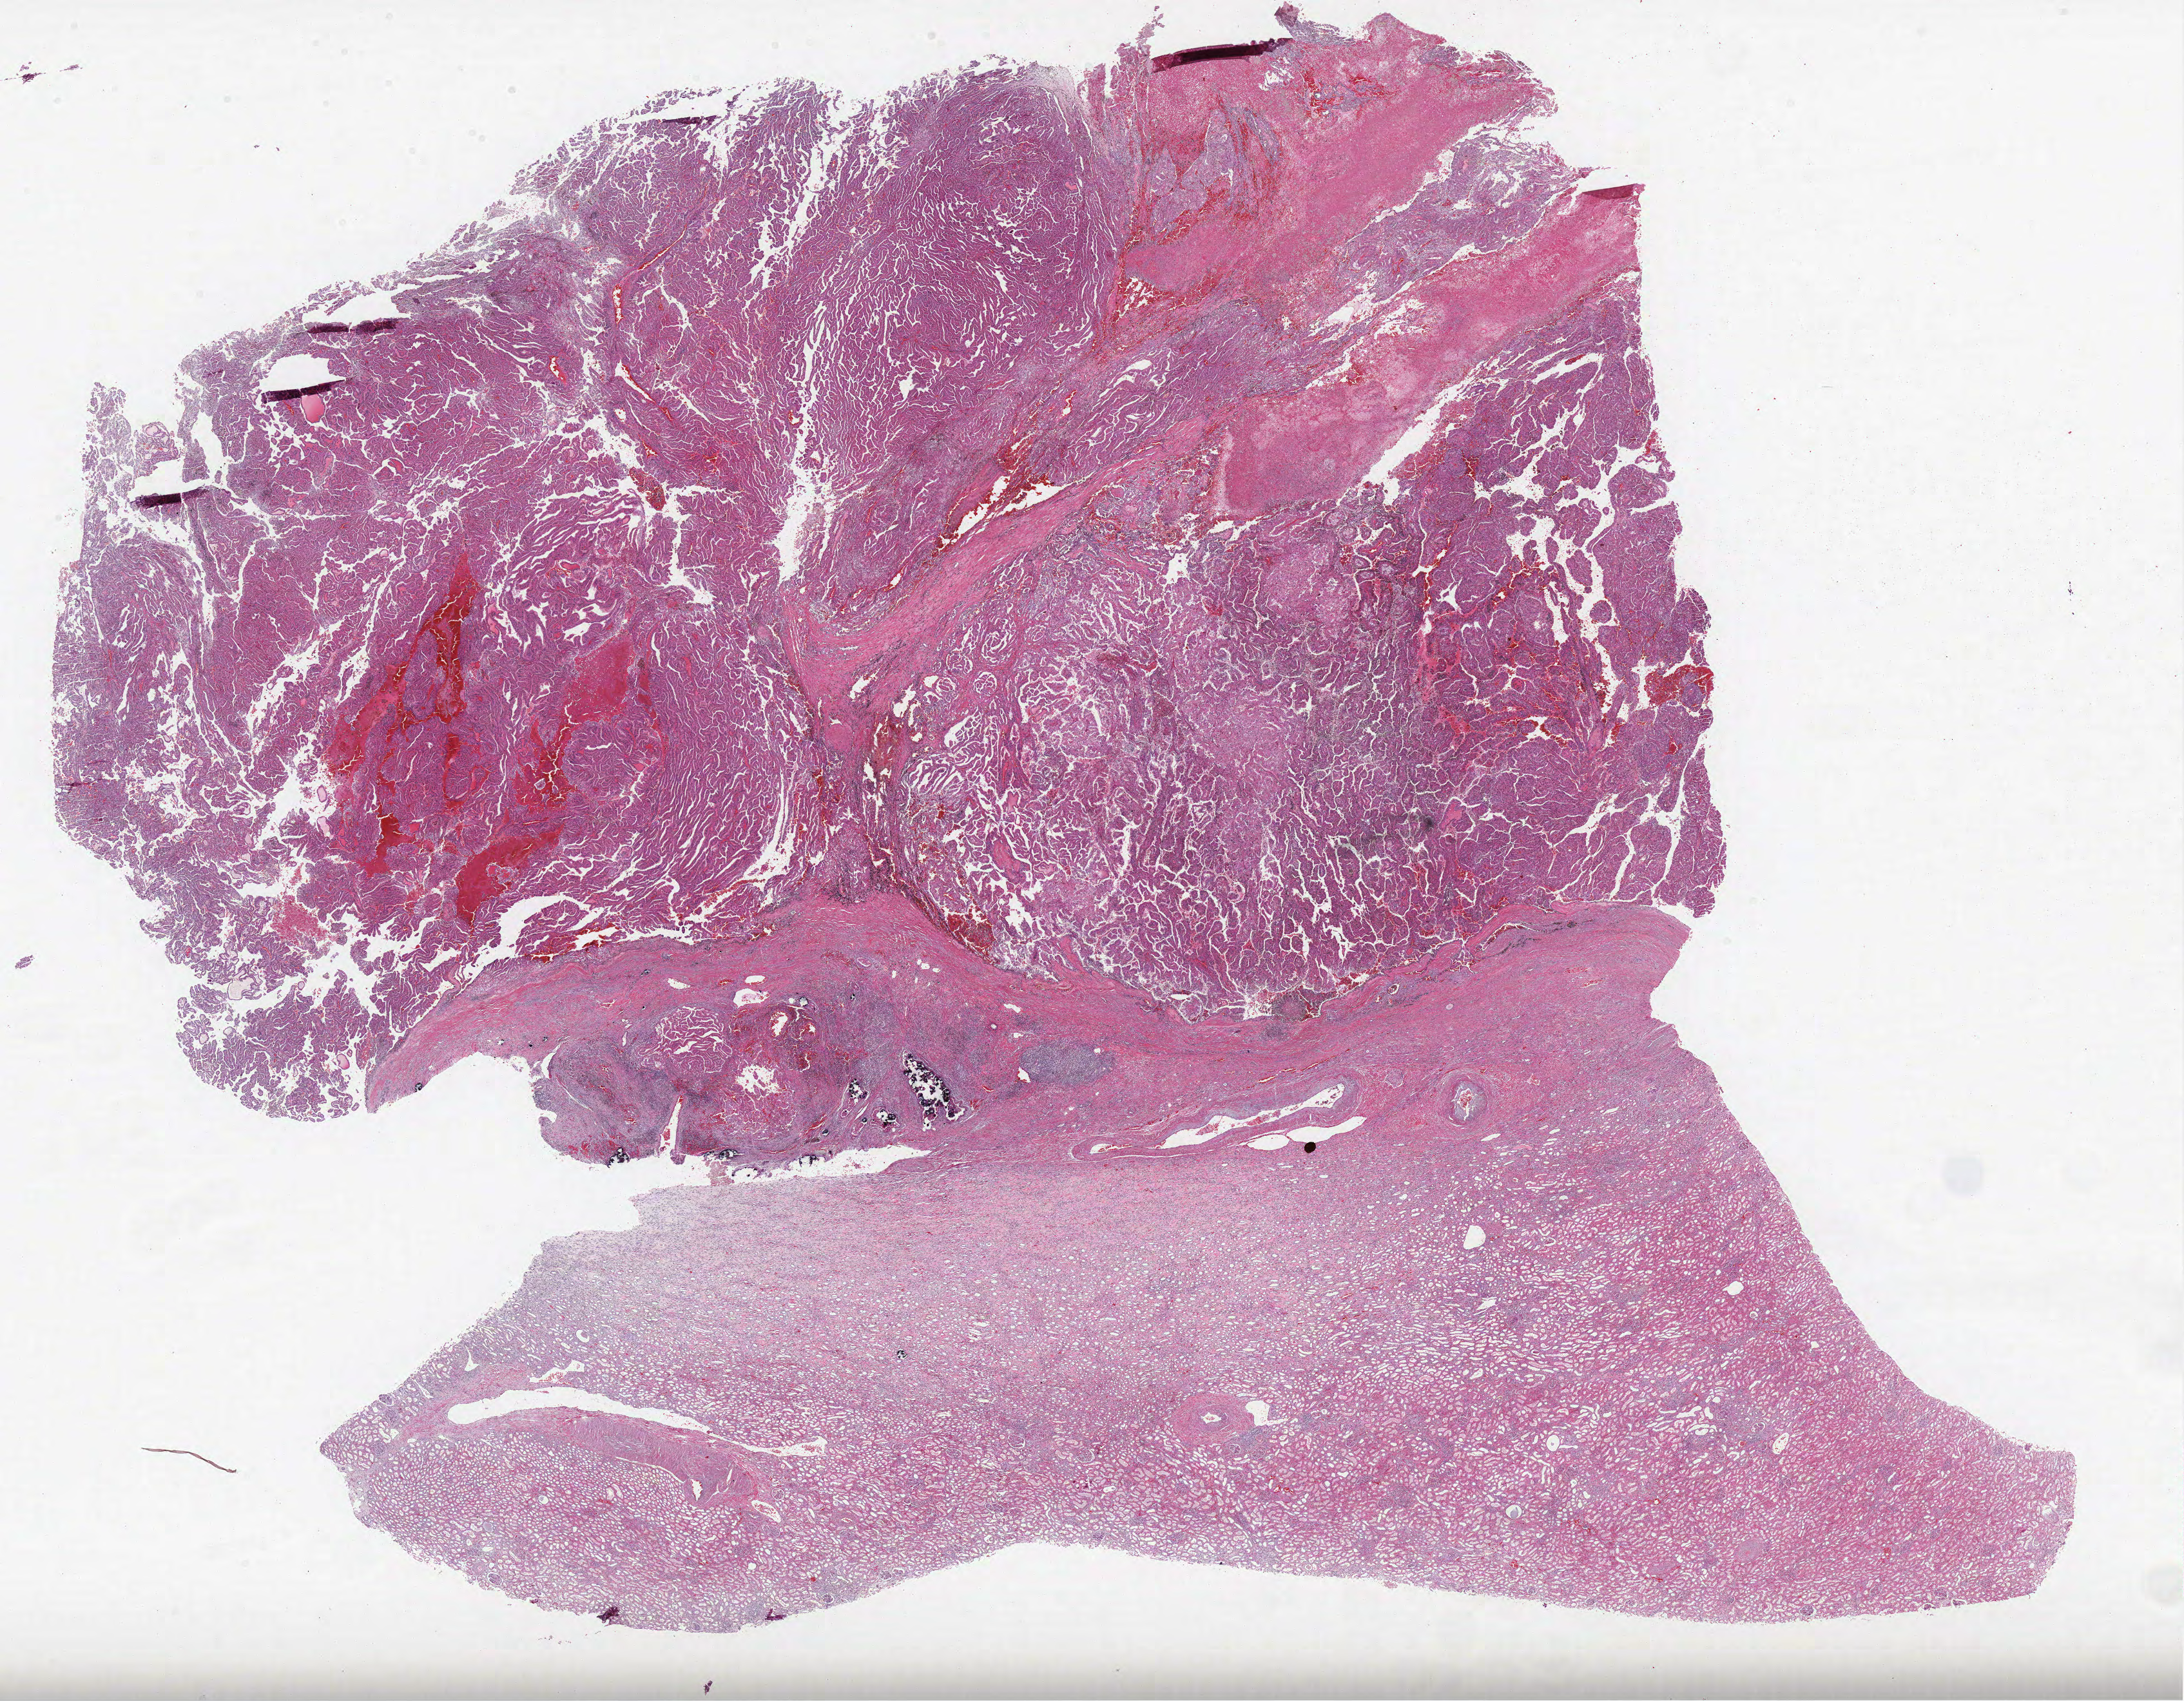
Digitized H&E tissue section (whole slide) — whole scanned area (about 27.1 x 21.1 mm, from a 40x scan) shown as a low-resolution overview. FFPE section. Sample: primary tumour, kidney. Male patient; age at initial diagnosis 73 years.
Laterality: left. AJCC pathologic stage: III. Pathologic diagnosis: Papillary adenocarcinoma, NOS.